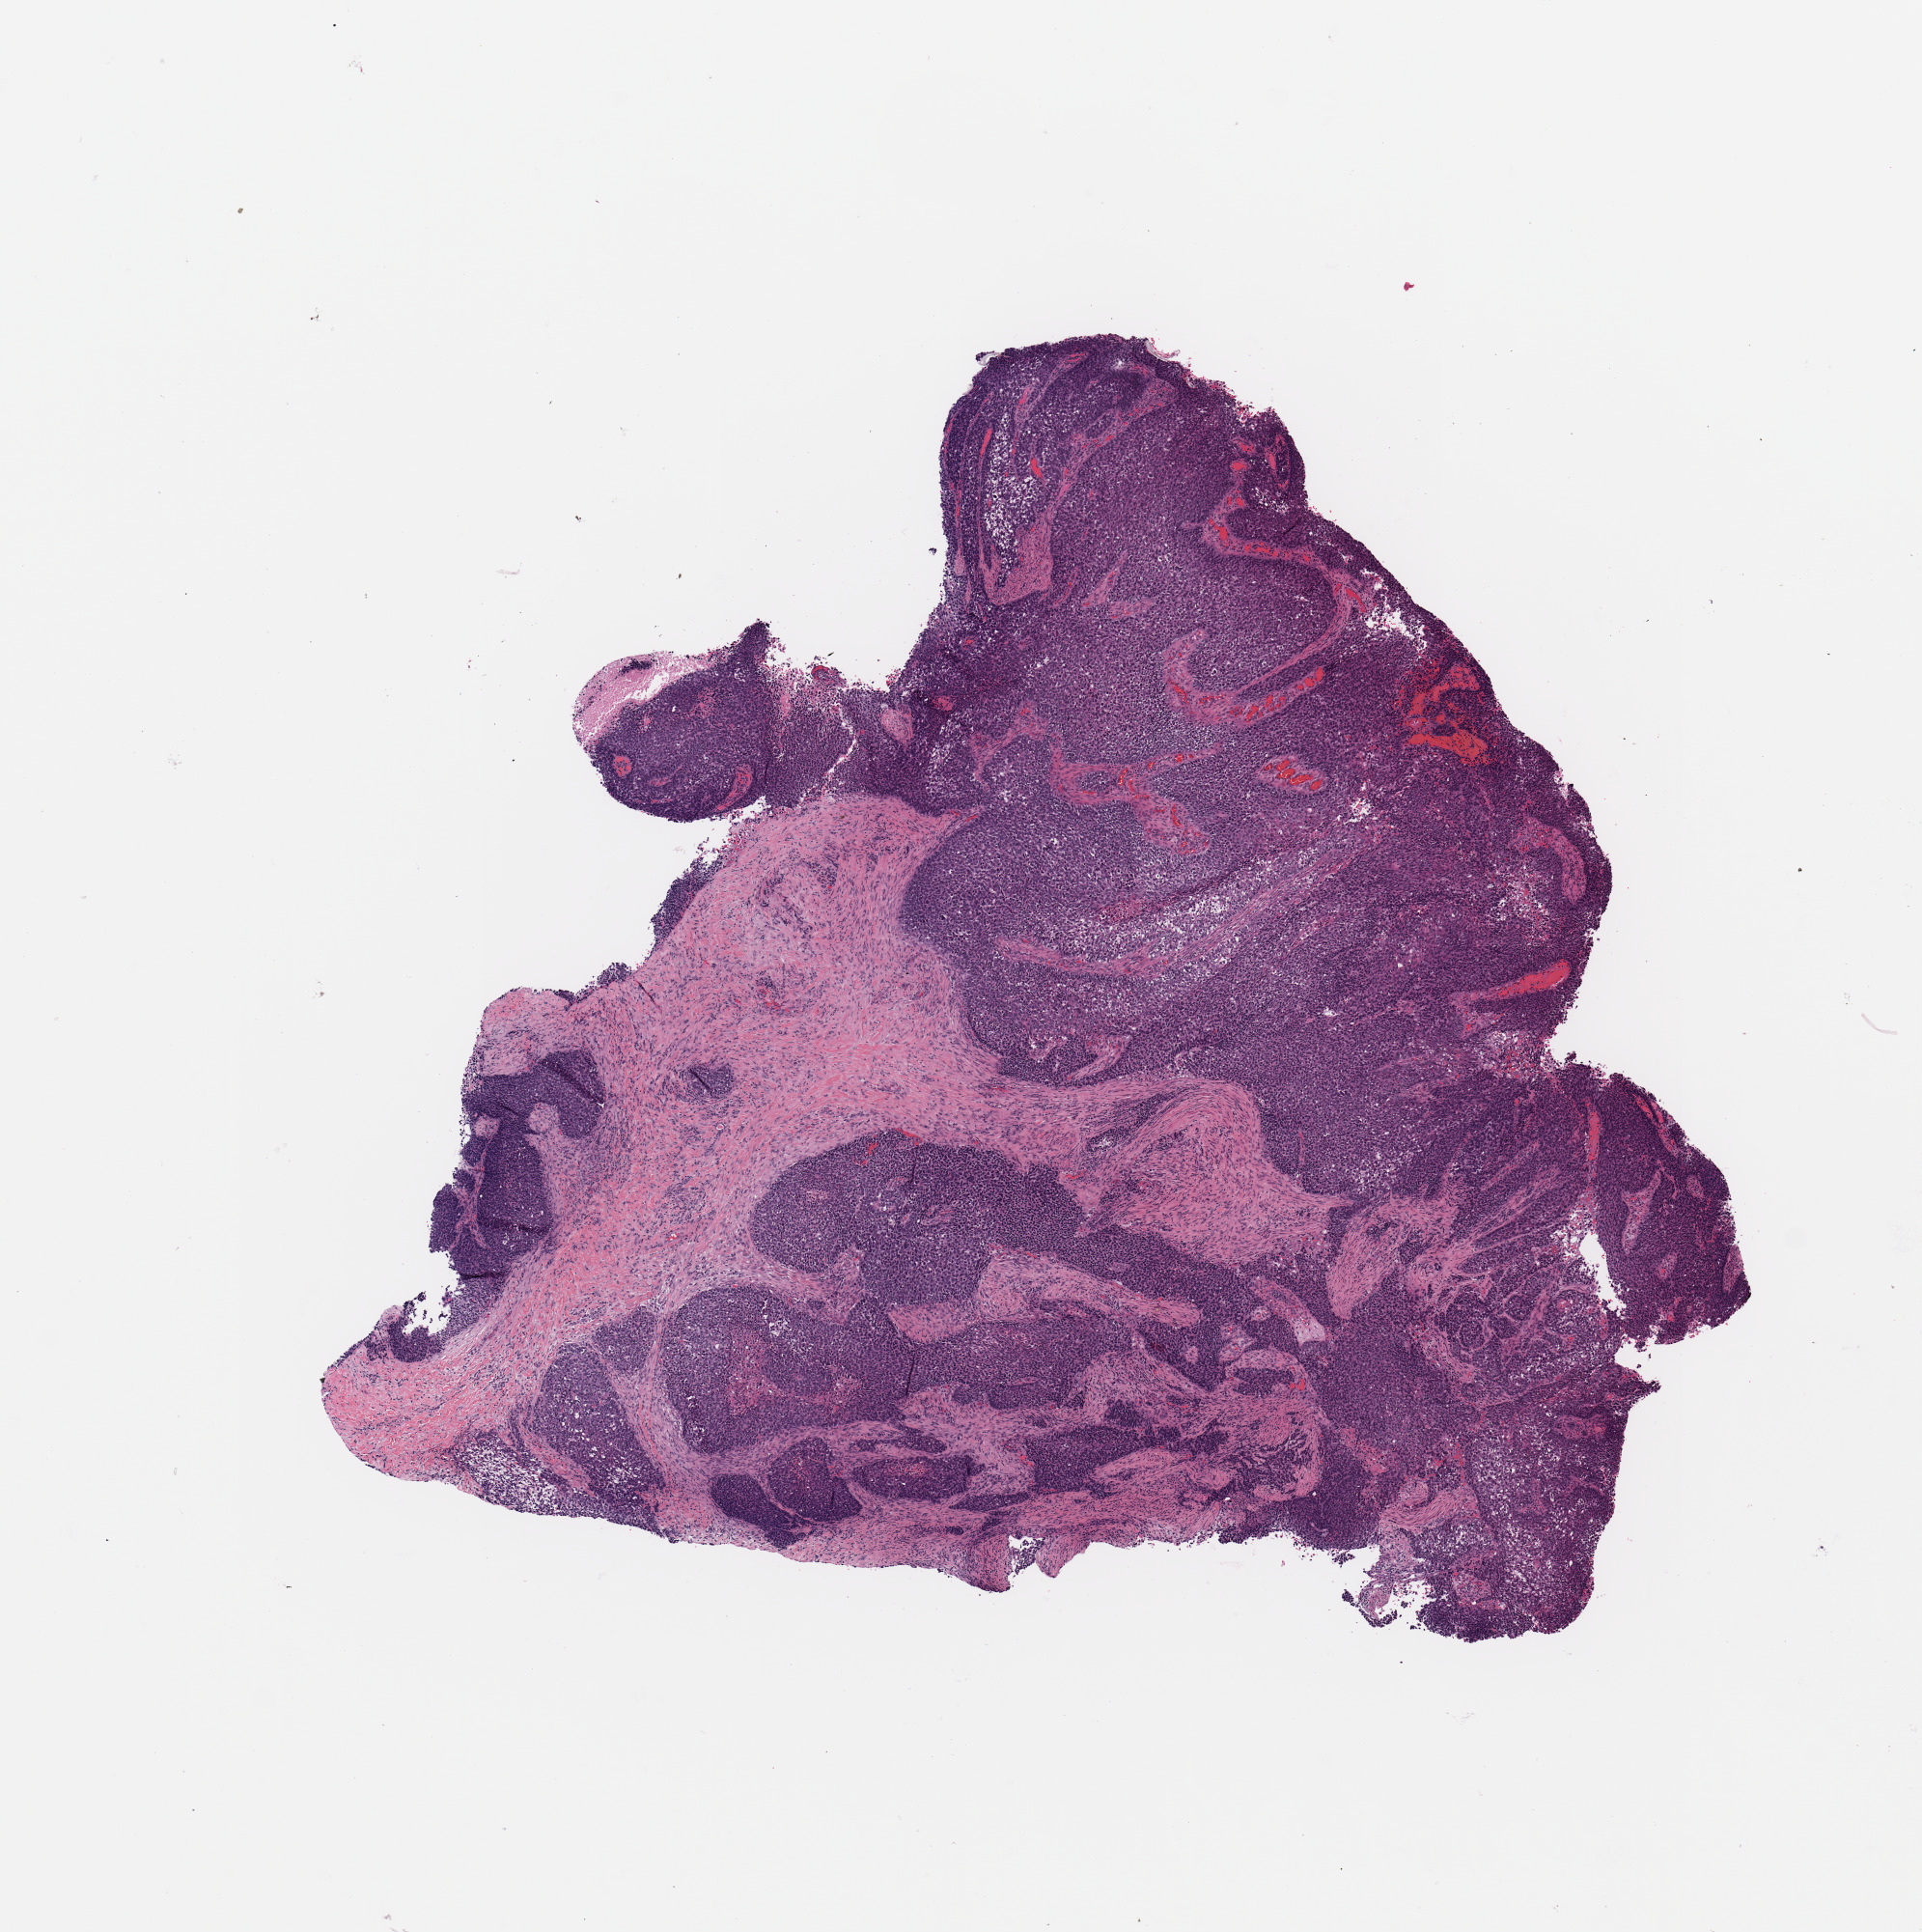
Whole-slide histology image, H&E, whole scanned area (about 7.9 x 7.9 mm, slide scanned at 20x) shown as a low-resolution overview; tumour tissue sample, sampled site: lung. Male, 63 y/o. Histologic grade: G2 (moderately differentiated). Pathologist review of this section (percent, as recorded): tumour nuclei 80%, necrosis 2%.
Diagnosis: Squamous cell carcinoma, NOS. Primary tumour site (as recorded): right upper lobe. AJCC pathologic stage: IIA.